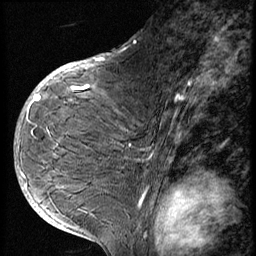
Breast MRI (dynamic contrast-enhanced), one sagittal slice. Slice 35 of 56 in the series (ordered by position). 3 images stored at this slice position (order not interpretable as contrast timing). 1.5 T. TE 4.2 ms, TR 9 ms. 2.5 mm slice thickness. 256 × 256 image matrix, field of view 180 × 180 mm. Patient: female, 49 years. Case-level facts recorded for this patient, not image findings: setting: breast cancer imaged before/during neoadjuvant chemotherapy; receptor status: HER2-positive.
Annotated regions visible in this slice (semi-automatic segmentation, software-assisted and operator-edited):
- analysis volume of interest (the breast-tissue region the enhancement analysis was run in; not a lesion): box from (x=37, y=85) to (x=128, y=207) px
- tumour enhancement mask (voxels above the 140 % enhancement threshold inside the analysis volume of interest): (x=37, y=86)–(x=90, y=101)